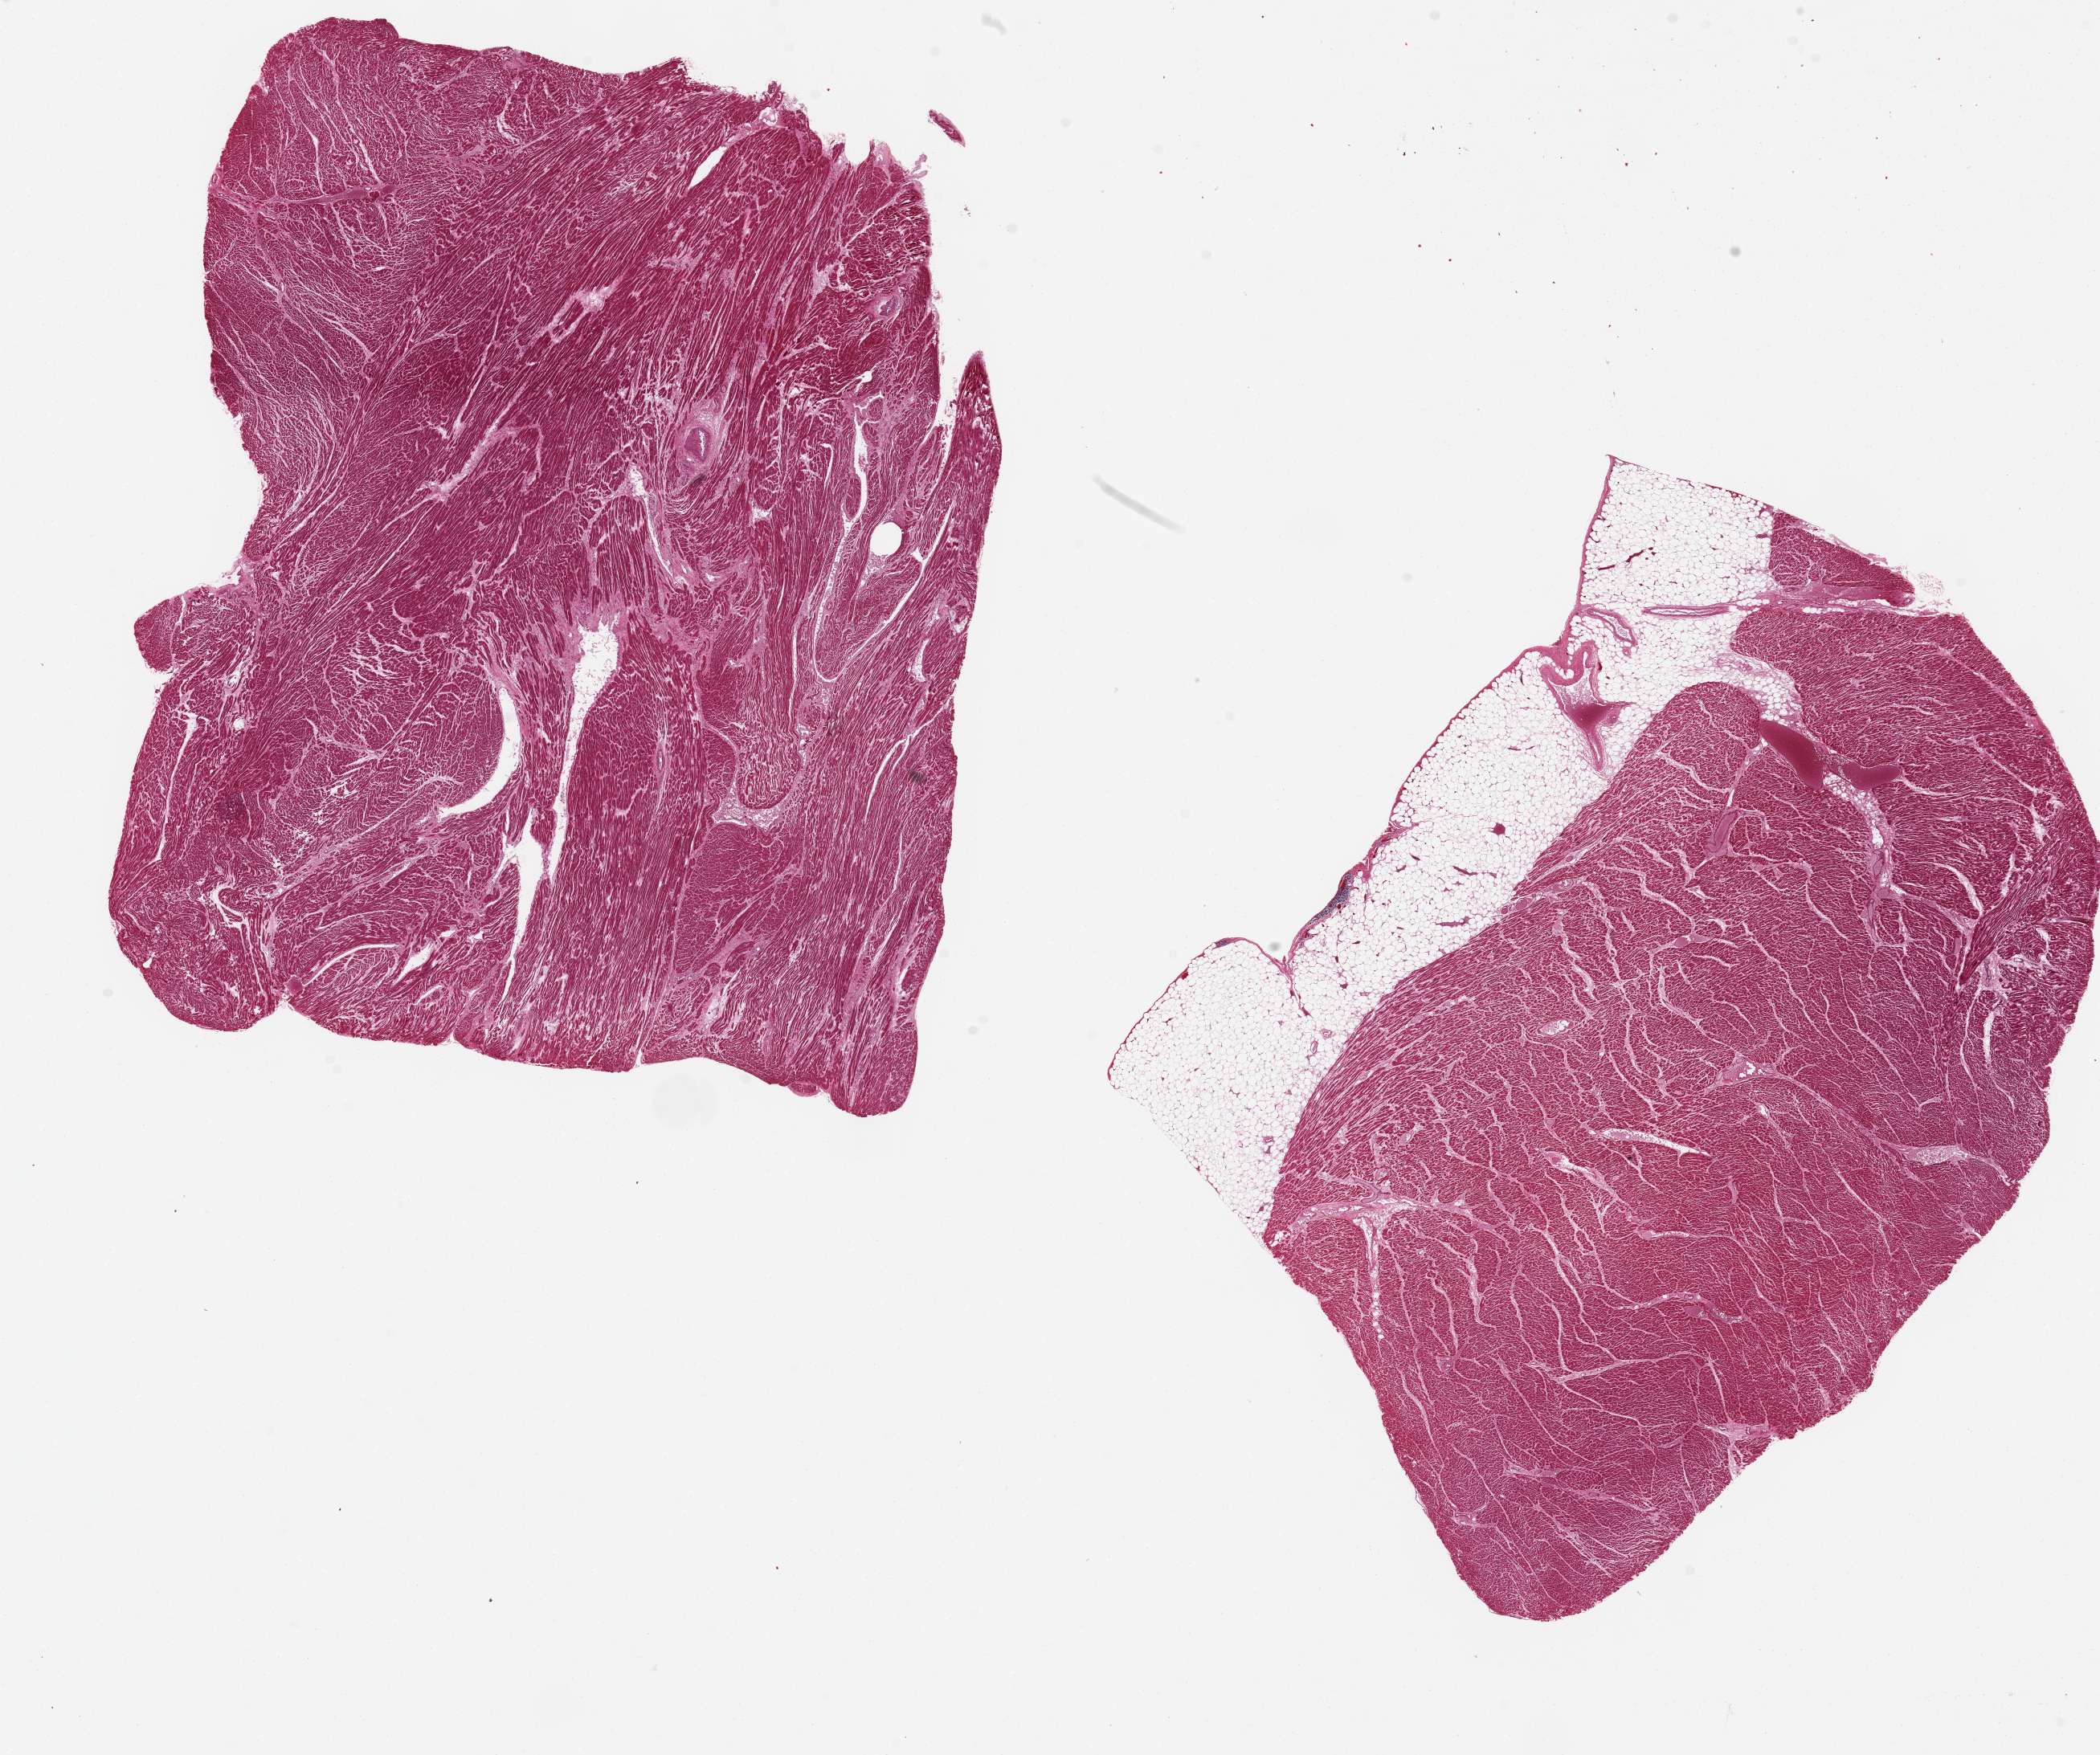
Hematoxylin and eosin (H&E) whole-slide image — a low-resolution overview of the entire scanned area, about 20.7 x 17.3 mm, PAXgene-fixed, paraffin-embedded tissue, sampled site (target tissue): heart, tissue donor sample. Donor: male.
• review note (as recorded): 2 ~9x7mm aliquots, patchy ischemic changes (contraction bands) noted. 8.5x1.5mm layer of fat along edge of one aliquot